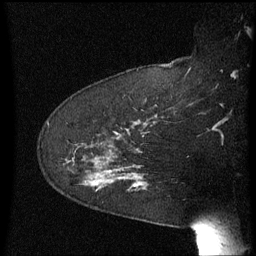
Breast MRI (dynamic contrast-enhanced), one sagittal slice. Position 46 of 60 along the scan axis. Dynamic contrast-enhanced series, image 2 of 3 at this slice position (ordered by acquisition). 1.5 T. TE 4.2 ms, TR 8.4 ms. 2.3 mm slice thickness. 256 × 256 image matrix, field of view 200 × 200 mm. Female patient, age 64 years. From the clinical record (not read from this slice): setting: breast cancer imaged before/during neoadjuvant chemotherapy; receptor status: HER2-positive.
Outlined on this slice (semi-automatically segmented with operator editing):
- analysis volume of interest (the breast-tissue region the enhancement analysis was run in; not a lesion): bounding box <68,158,148,211> (left, top, right, bottom; pixels)
- tumour enhancement mask (voxels above the 70 % enhancement threshold inside the analysis volume of interest): <135,184,137,187>